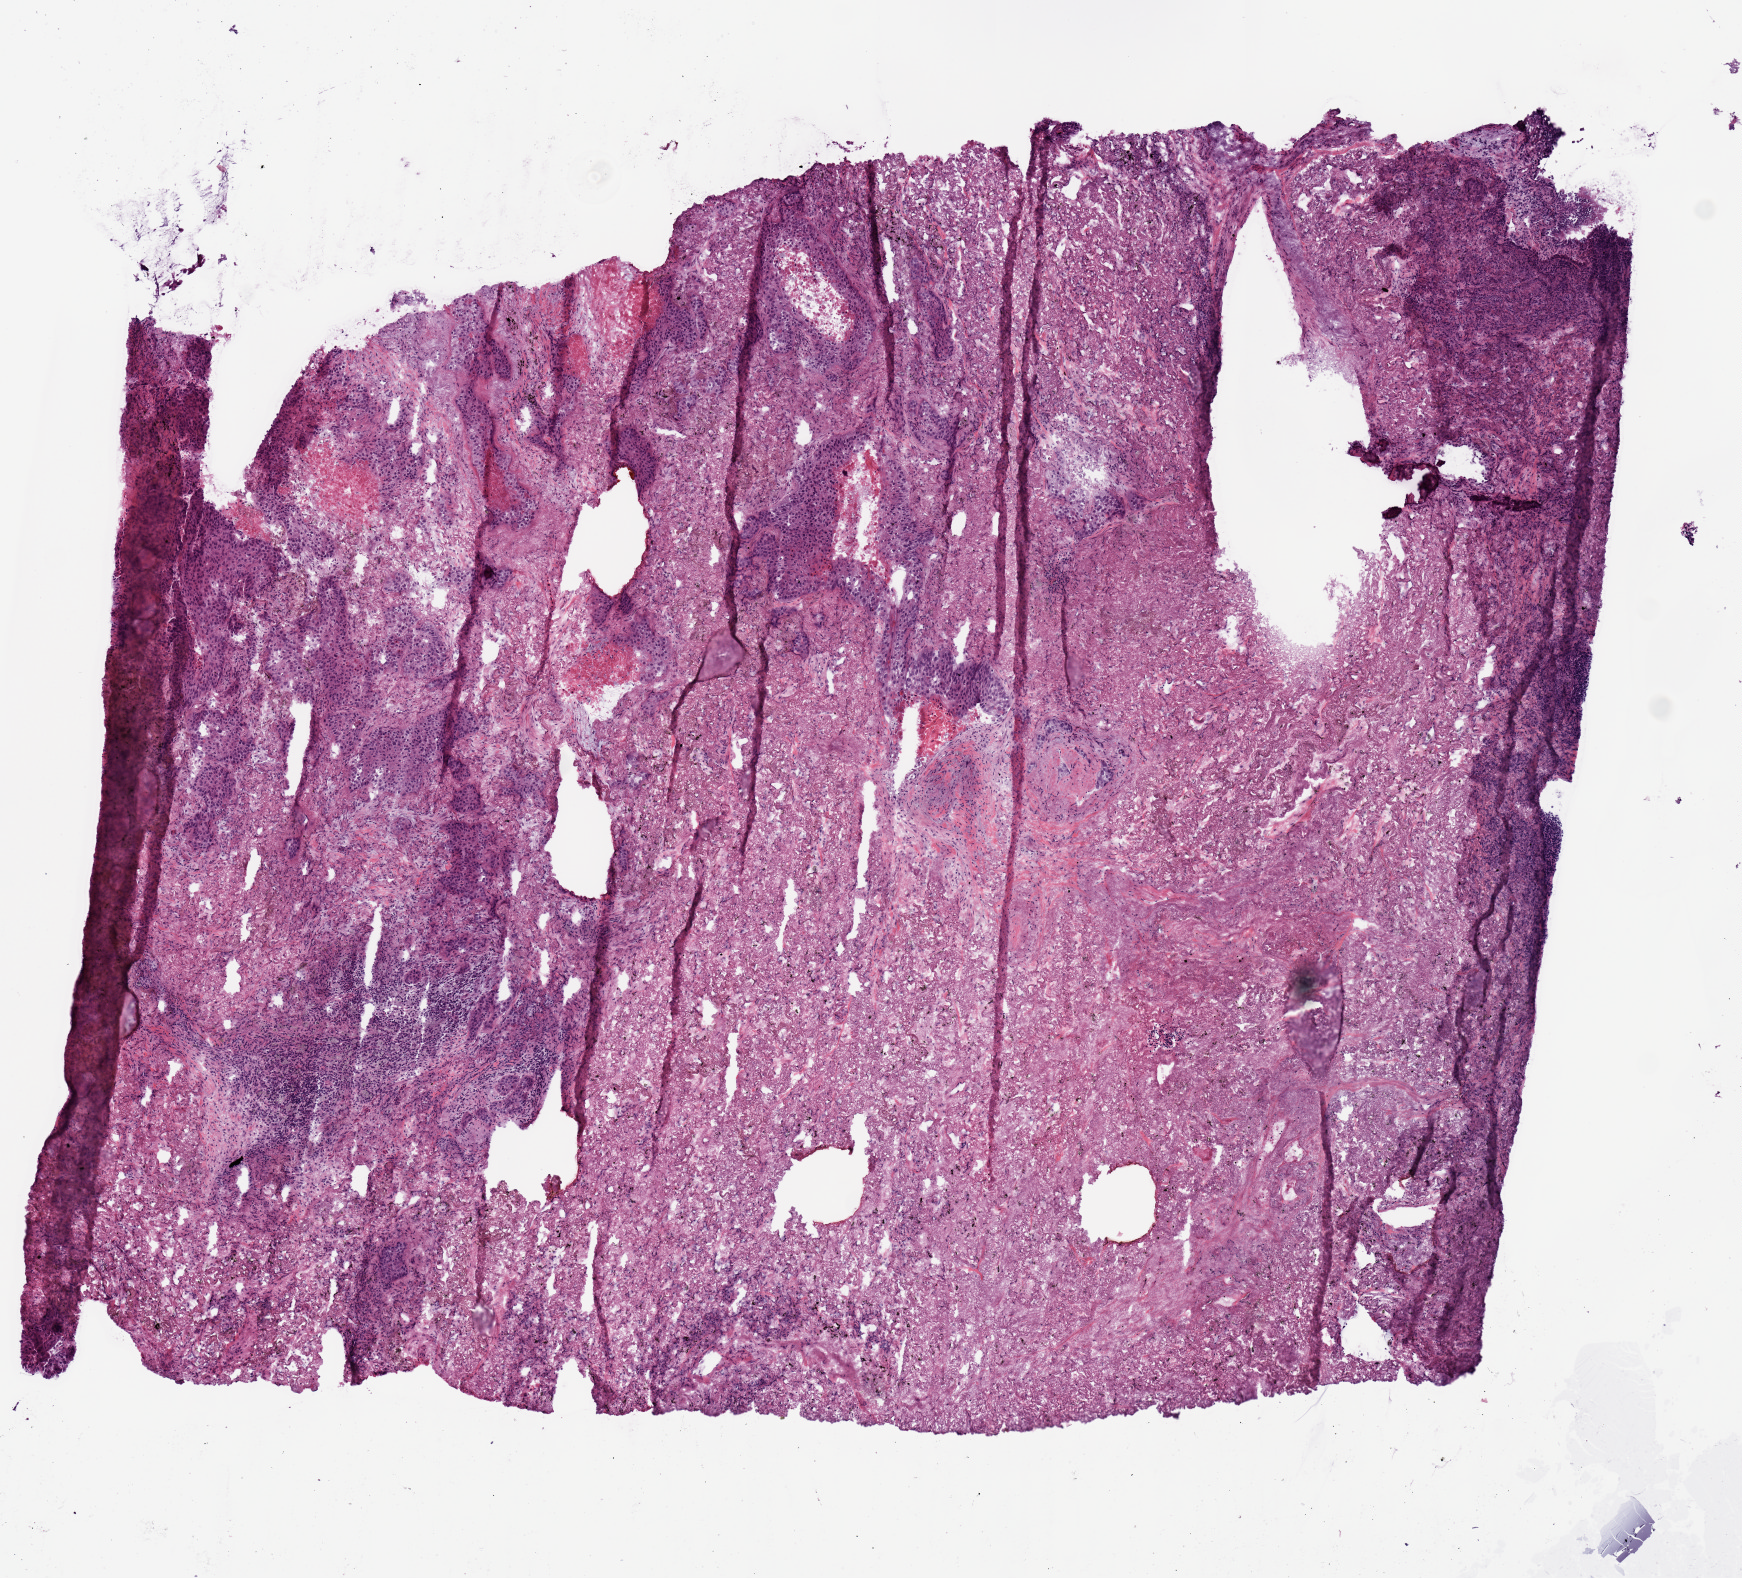
Whole-slide histology image, H&E-stained — low-resolution overview of the scanned area, about 6.9 x 6.2 mm (acquisition: 20x scan); frozen section; lung, primary tumour sample. Female patient; age at initial diagnosis 68 years.
Diagnosis: Squamous cell carcinoma, NOS (upper lobe, lung).